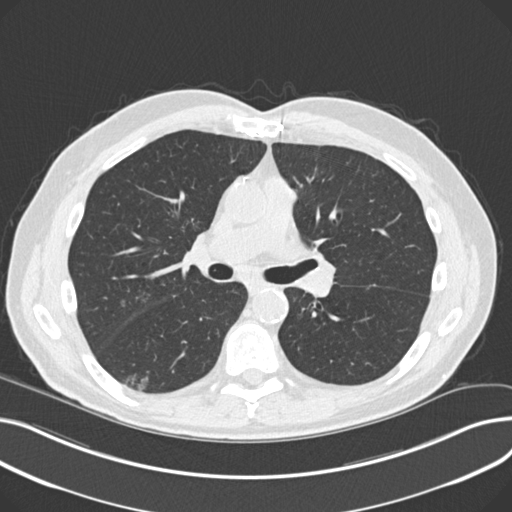
Low-dose screening chest CT, one axial slice; position 127 of 230 along the scan axis; 120 kVp; lung window (W 1500 / L -600 HU); 2 mm slice thickness; 512 × 512 image matrix.
Outlined on this slice (expert manual segmentation):
- lesion 1 (nodule, lower lobe of right lung): bounding box [x1, y1, x2, y2] px = [123, 373, 149, 389]